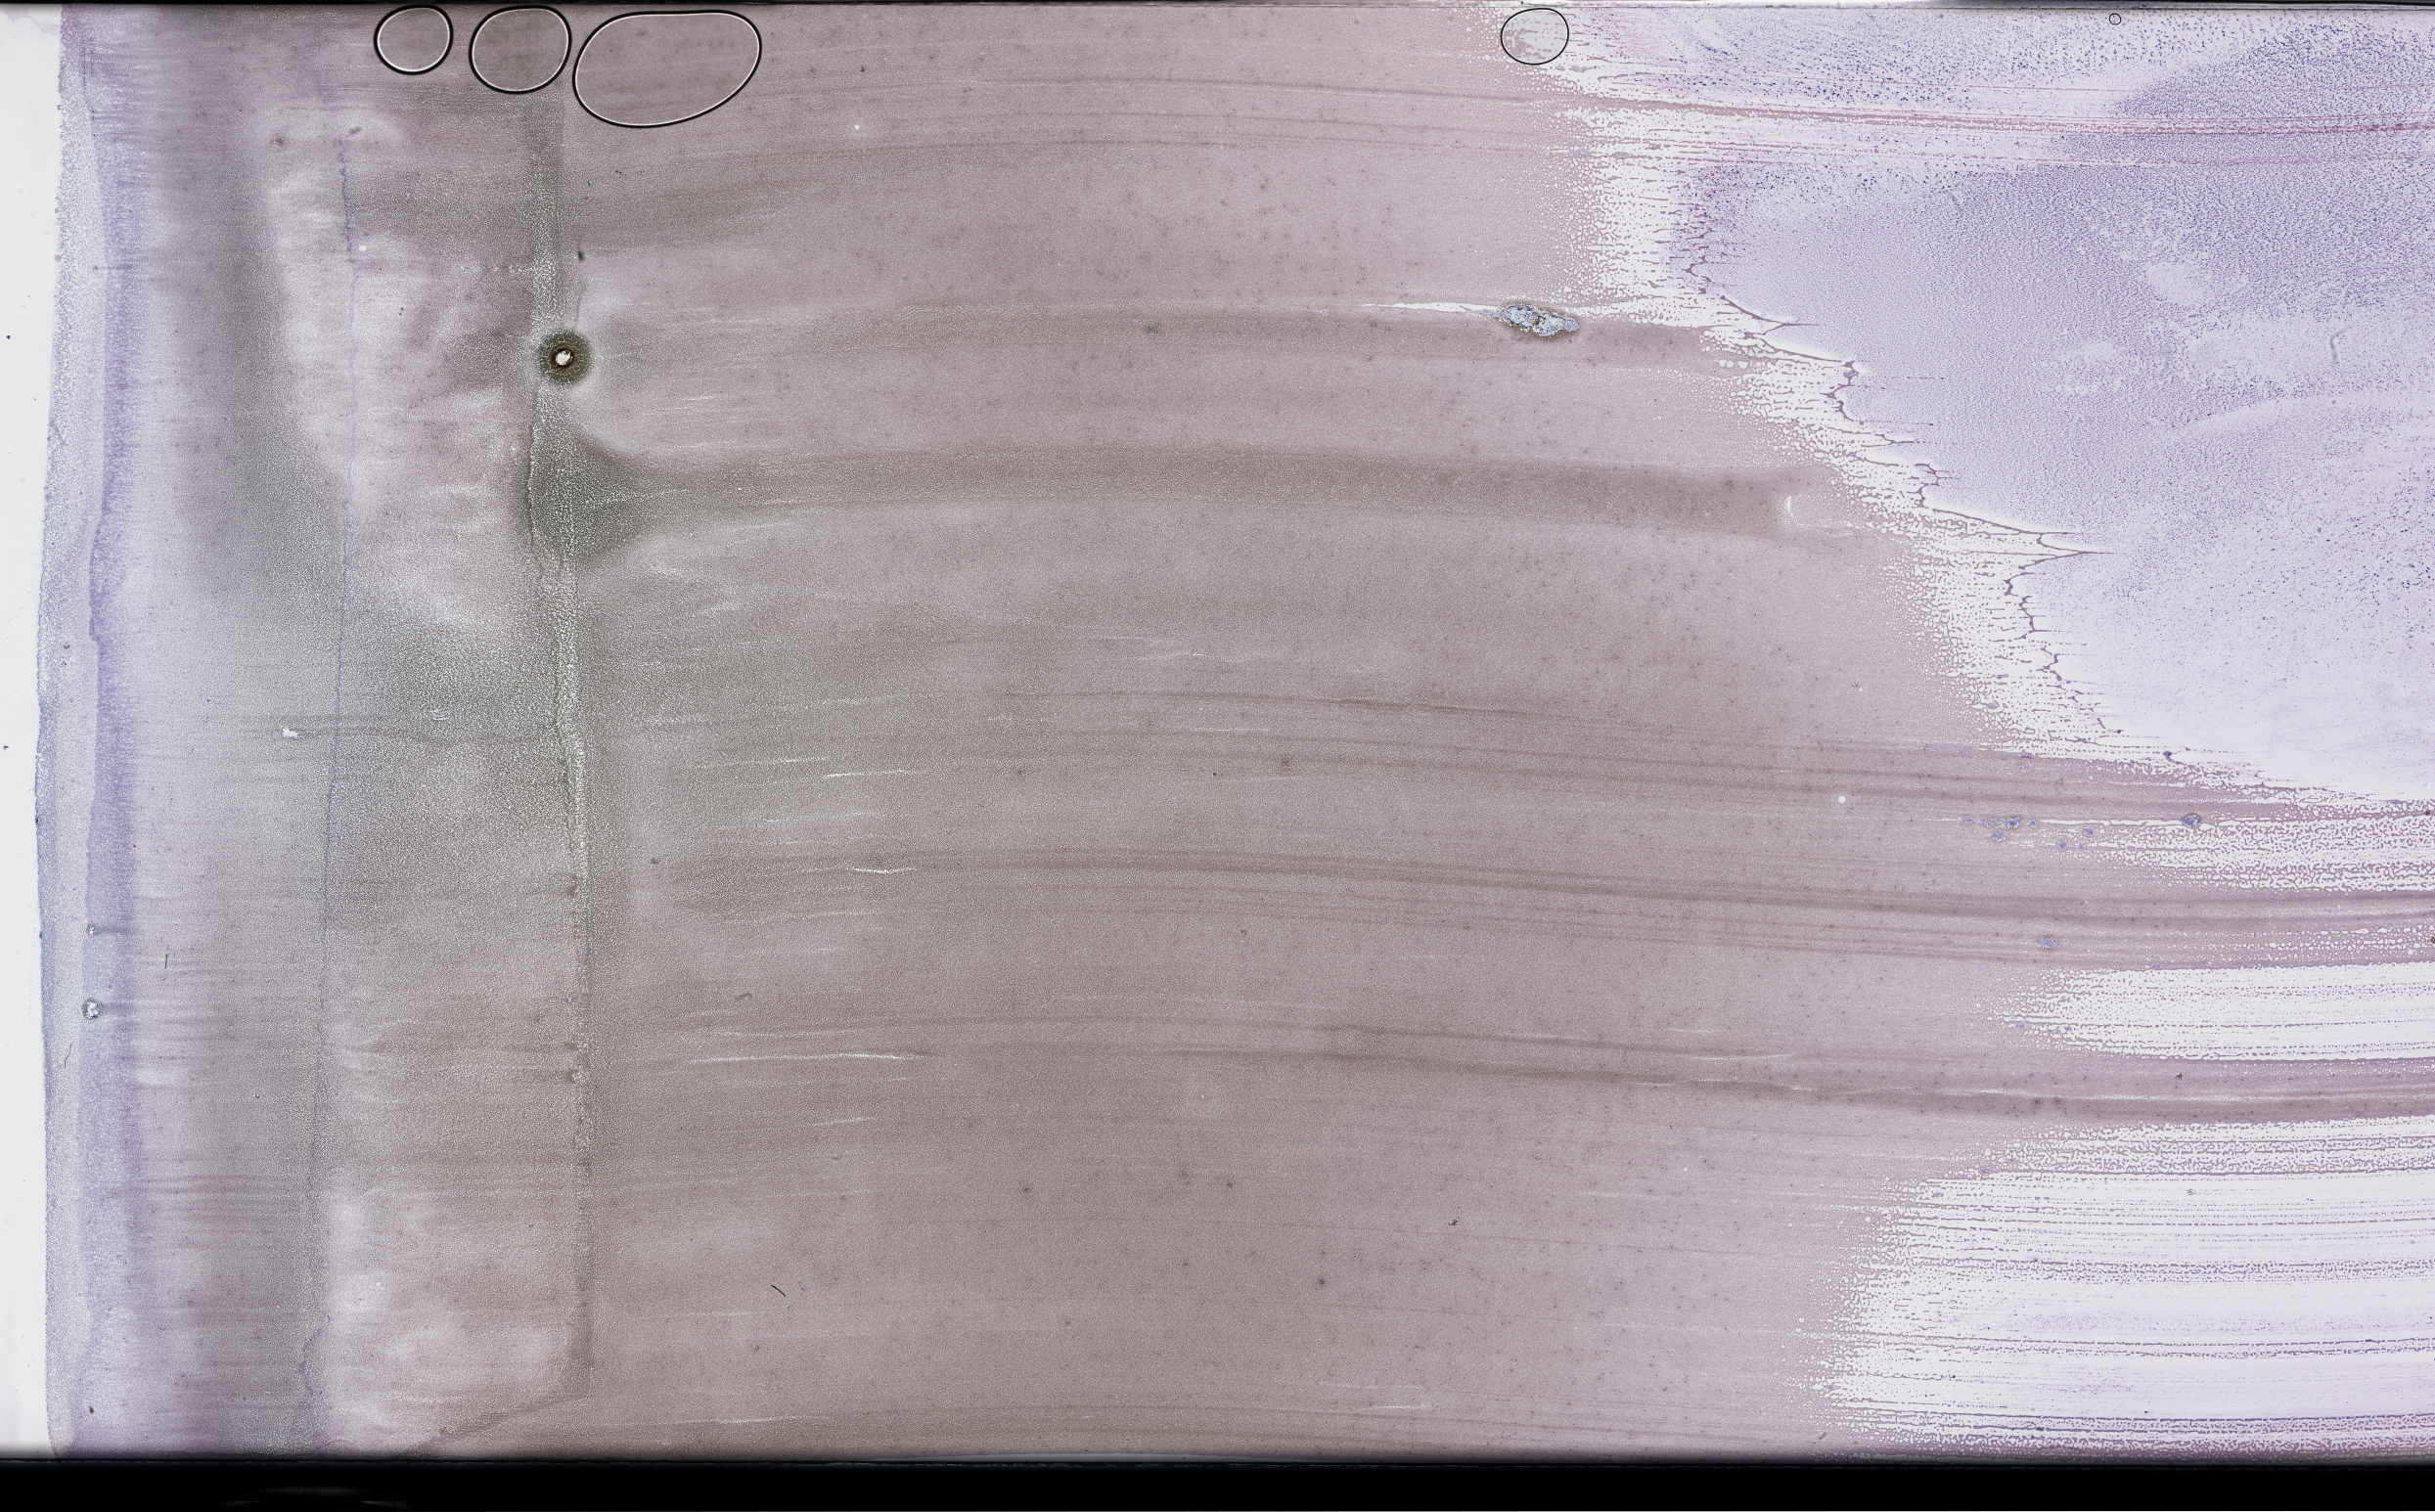
Wright-Giemsa-stained whole blood smear, whole-slide image — a low-resolution overview of the entire scanned area, about 40.2 x 25.0 mm, EDTA-anticoagulated smear. Patient sex: male.
- from a patient with: Plasma Cell Myeloma